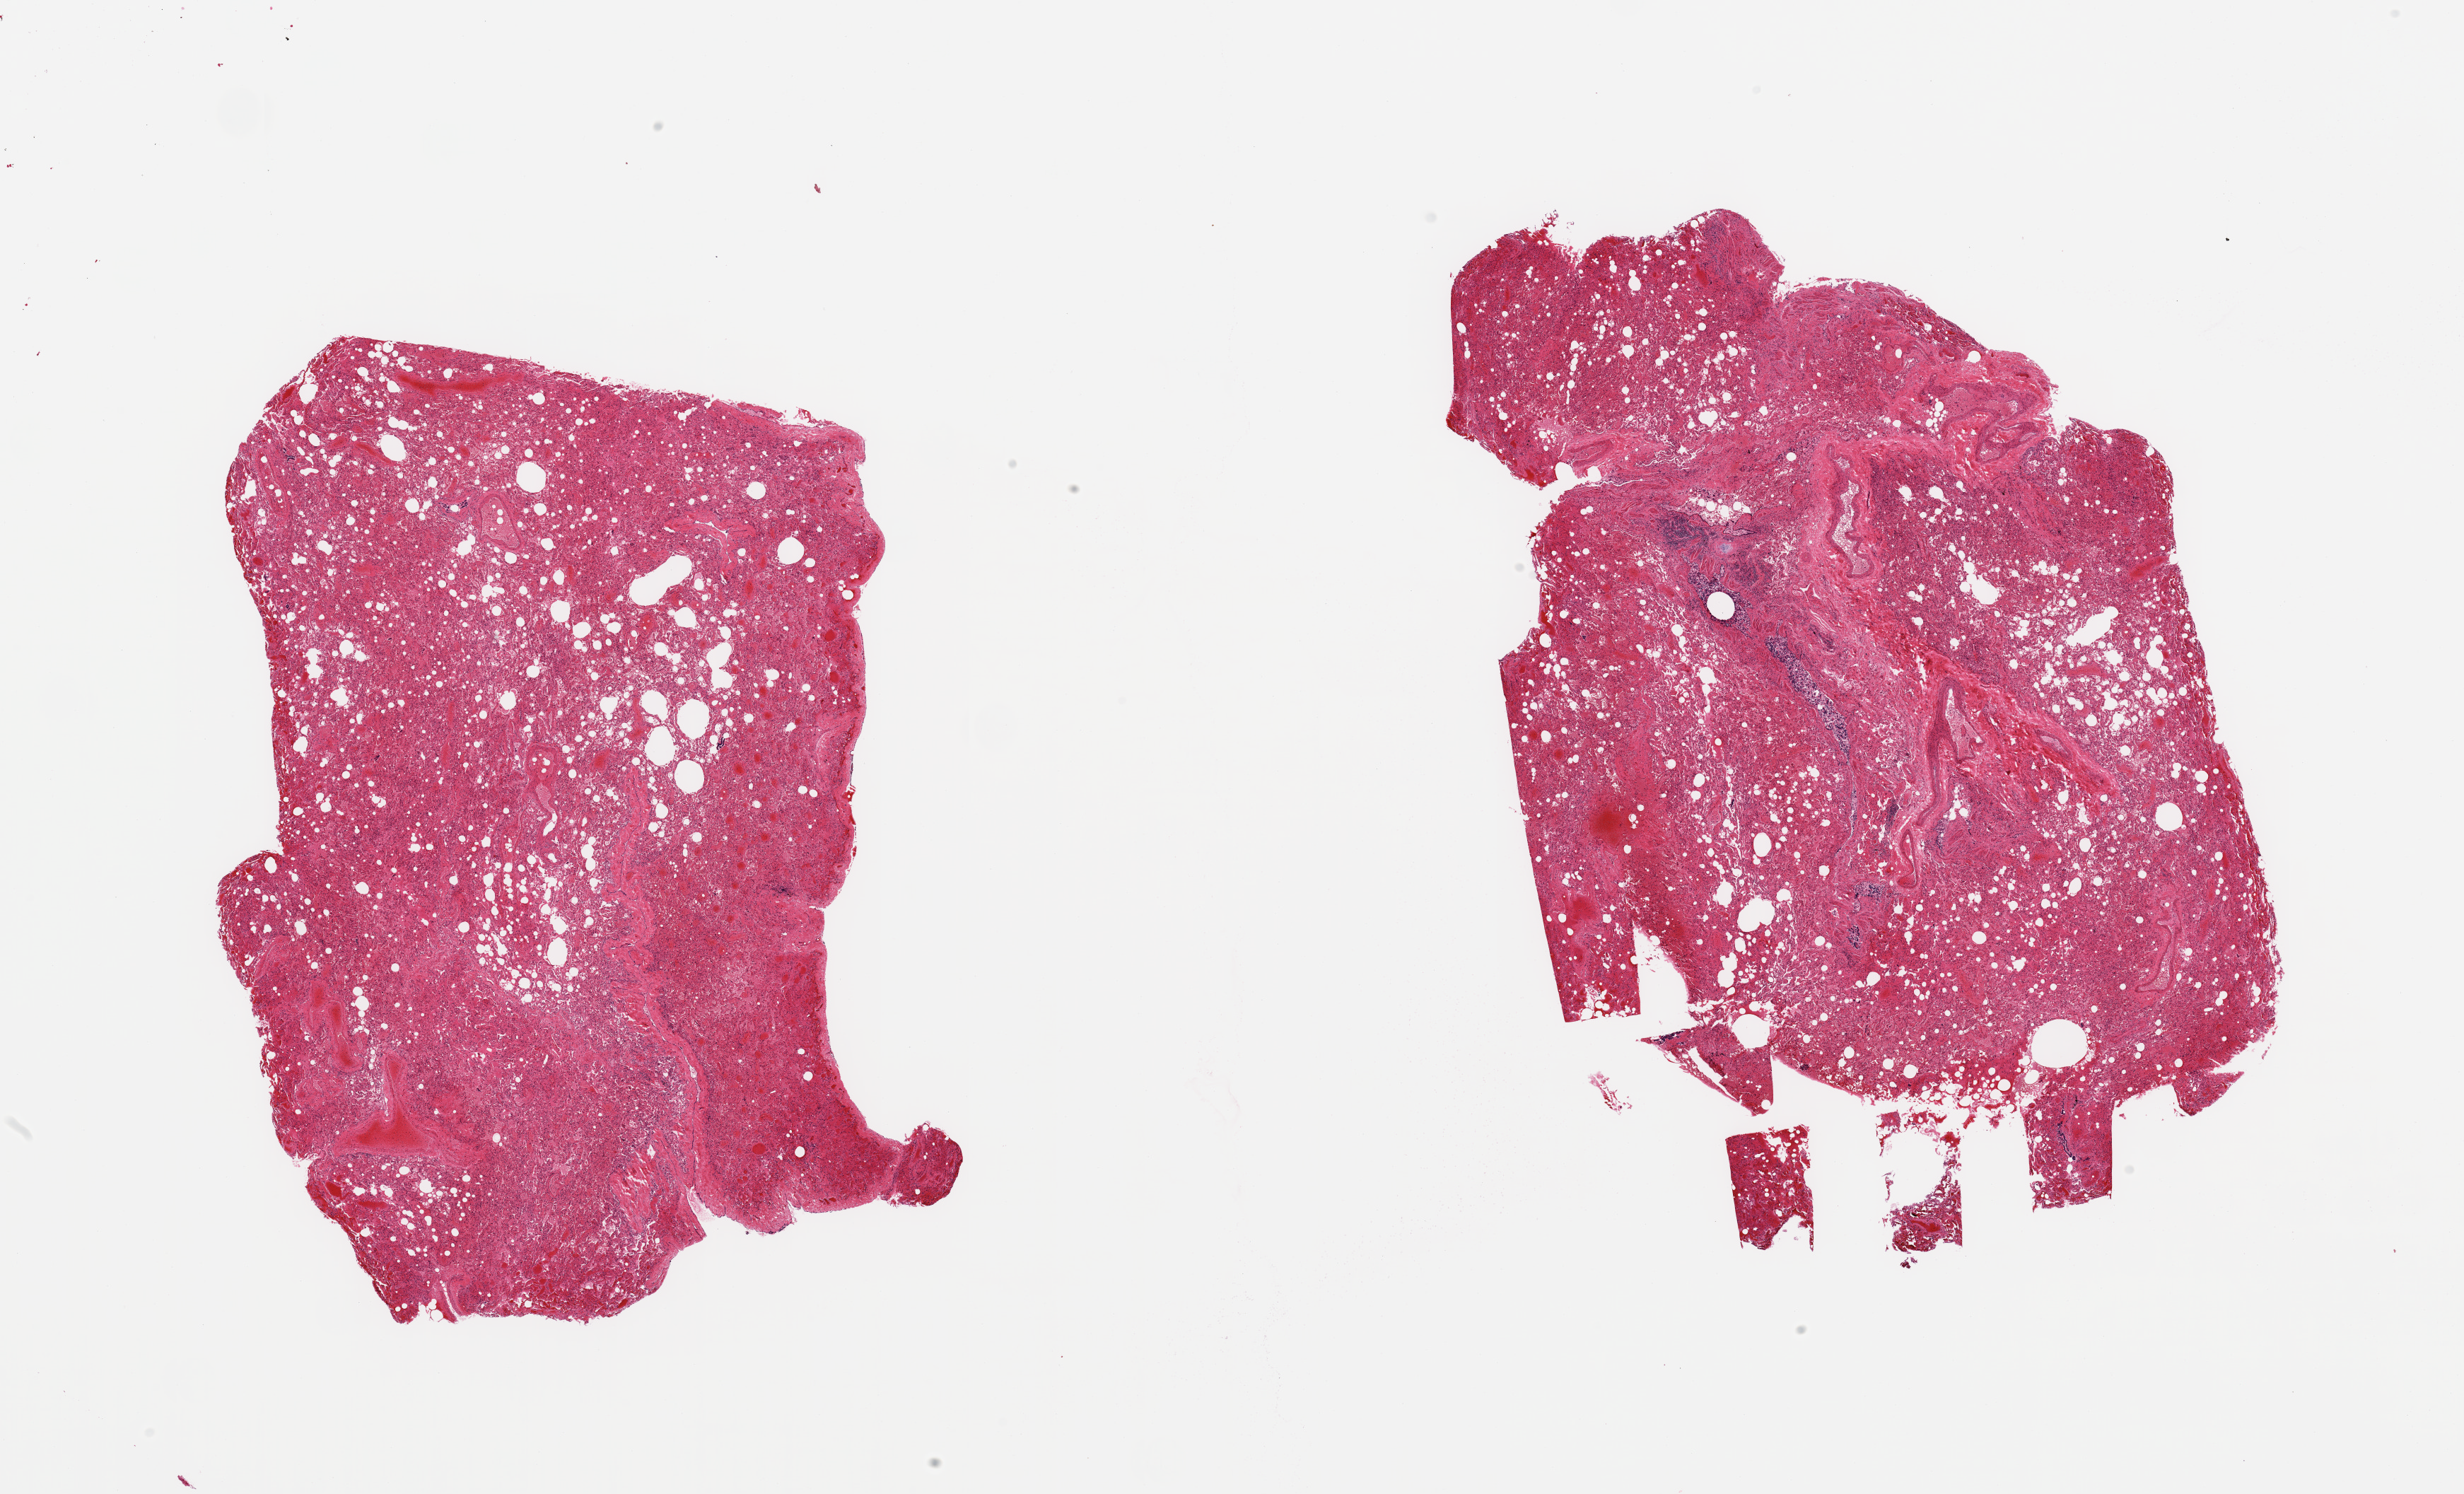
Digitized haematoxylin and eosin-stained section — shown as a low-resolution overview of the whole scanned area (about 27.6 x 16.7 mm, from a 20x scan), PAXgene-fixed, paraffin-embedded tissue, sampled site (target tissue): lung, donor tissue sample. Donor: female.
• review note (as recorded): 2 pieces, moderate edema;atalectatic